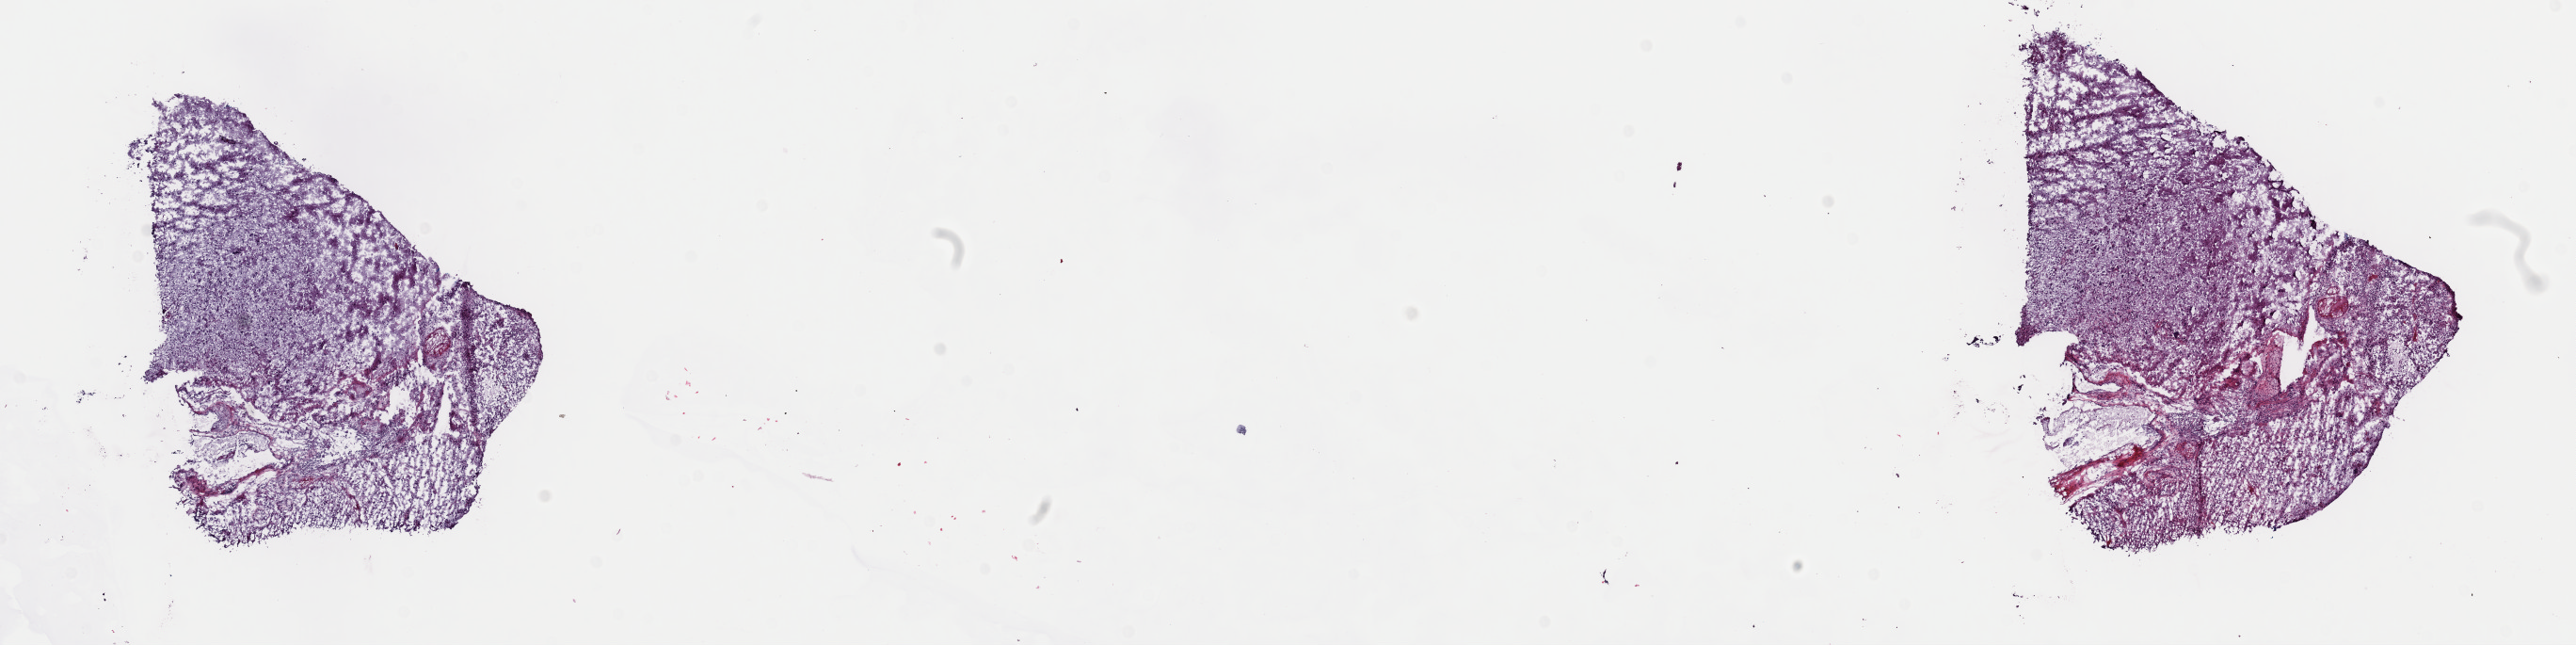
H&E whole-slide image — whole scanned area (about 21.6 x 5.4 mm) shown as a low-resolution overview, frozen section, sample: primary tumour, brain. Male, age 39 years at initial diagnosis. Pathologist review of this section (percent, as recorded): tumour cells 50%, tumour nuclei 80%, normal cells 5%, stromal cells 40%, necrosis 5%. Inflammatory infiltration, as recorded: lymphocyte infiltration 5%, monocyte infiltration 0%, neutrophil infiltration 0%.
• diagnosis: Glioblastoma